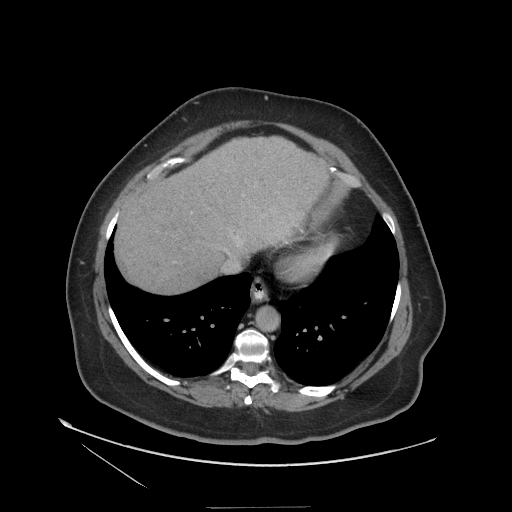
Contrast-enhanced abdominal CT (liver protocol), one axial slice. Position 100 of 127 along the scan axis. Reconstruction kernel STANDARD. Soft-tissue window (W 400 / L 40 HU). 2.5 mm slice thickness. 512 × 512 image matrix, field of view 480 × 480 mm. From the clinical record (not read from this slice): diagnosis: hepatocellular carcinoma (patient treated with transarterial chemoembolisation; whether this scan precedes or follows treatment is not stated here); TNM stage (as recorded): Stage-II.
Annotated regions visible in this slice (semi-automatic segmentation, software-assisted and operator-edited):
- liver parenchyma outside the tumour (the mass and vessels are separate outlines, so this box may not span the whole liver): bounding box (x1, y1, x2, y2) in pixels: (116, 136, 330, 292)